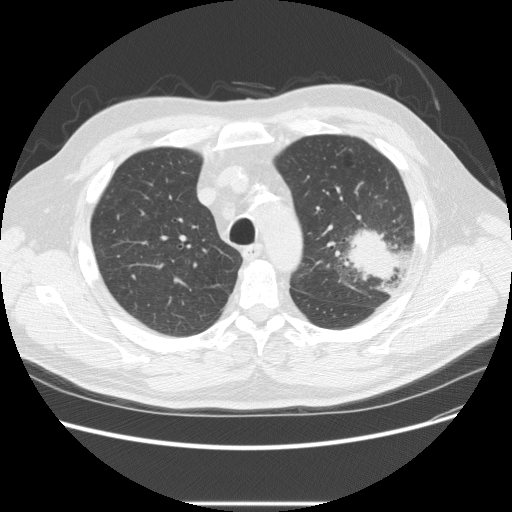
Low-dose screening chest CT, axial slice, baseline screening round, lung window (W 1500 / L -600 HU), 2.5 mm slice thickness, slice 61 of 233 in the series, 512 × 512 image matrix, field of view 380 × 380 mm. Male participant, aged 73 years at enrolment.
- Expert-annotated lung lesion, box from (x=332, y=215) to (x=416, y=286) px.
- The screening reader recorded 2 non-calcified nodules or masses ≥4 mm on this exam; which of them this box marks is not recorded.
- Later outcome: lung cancer diagnosed 11 days after this screen — bronchiolo-alveolar adenocarcinoma, NOS, other location, well differentiated (G1), stage IV (AJCC 6th edition).